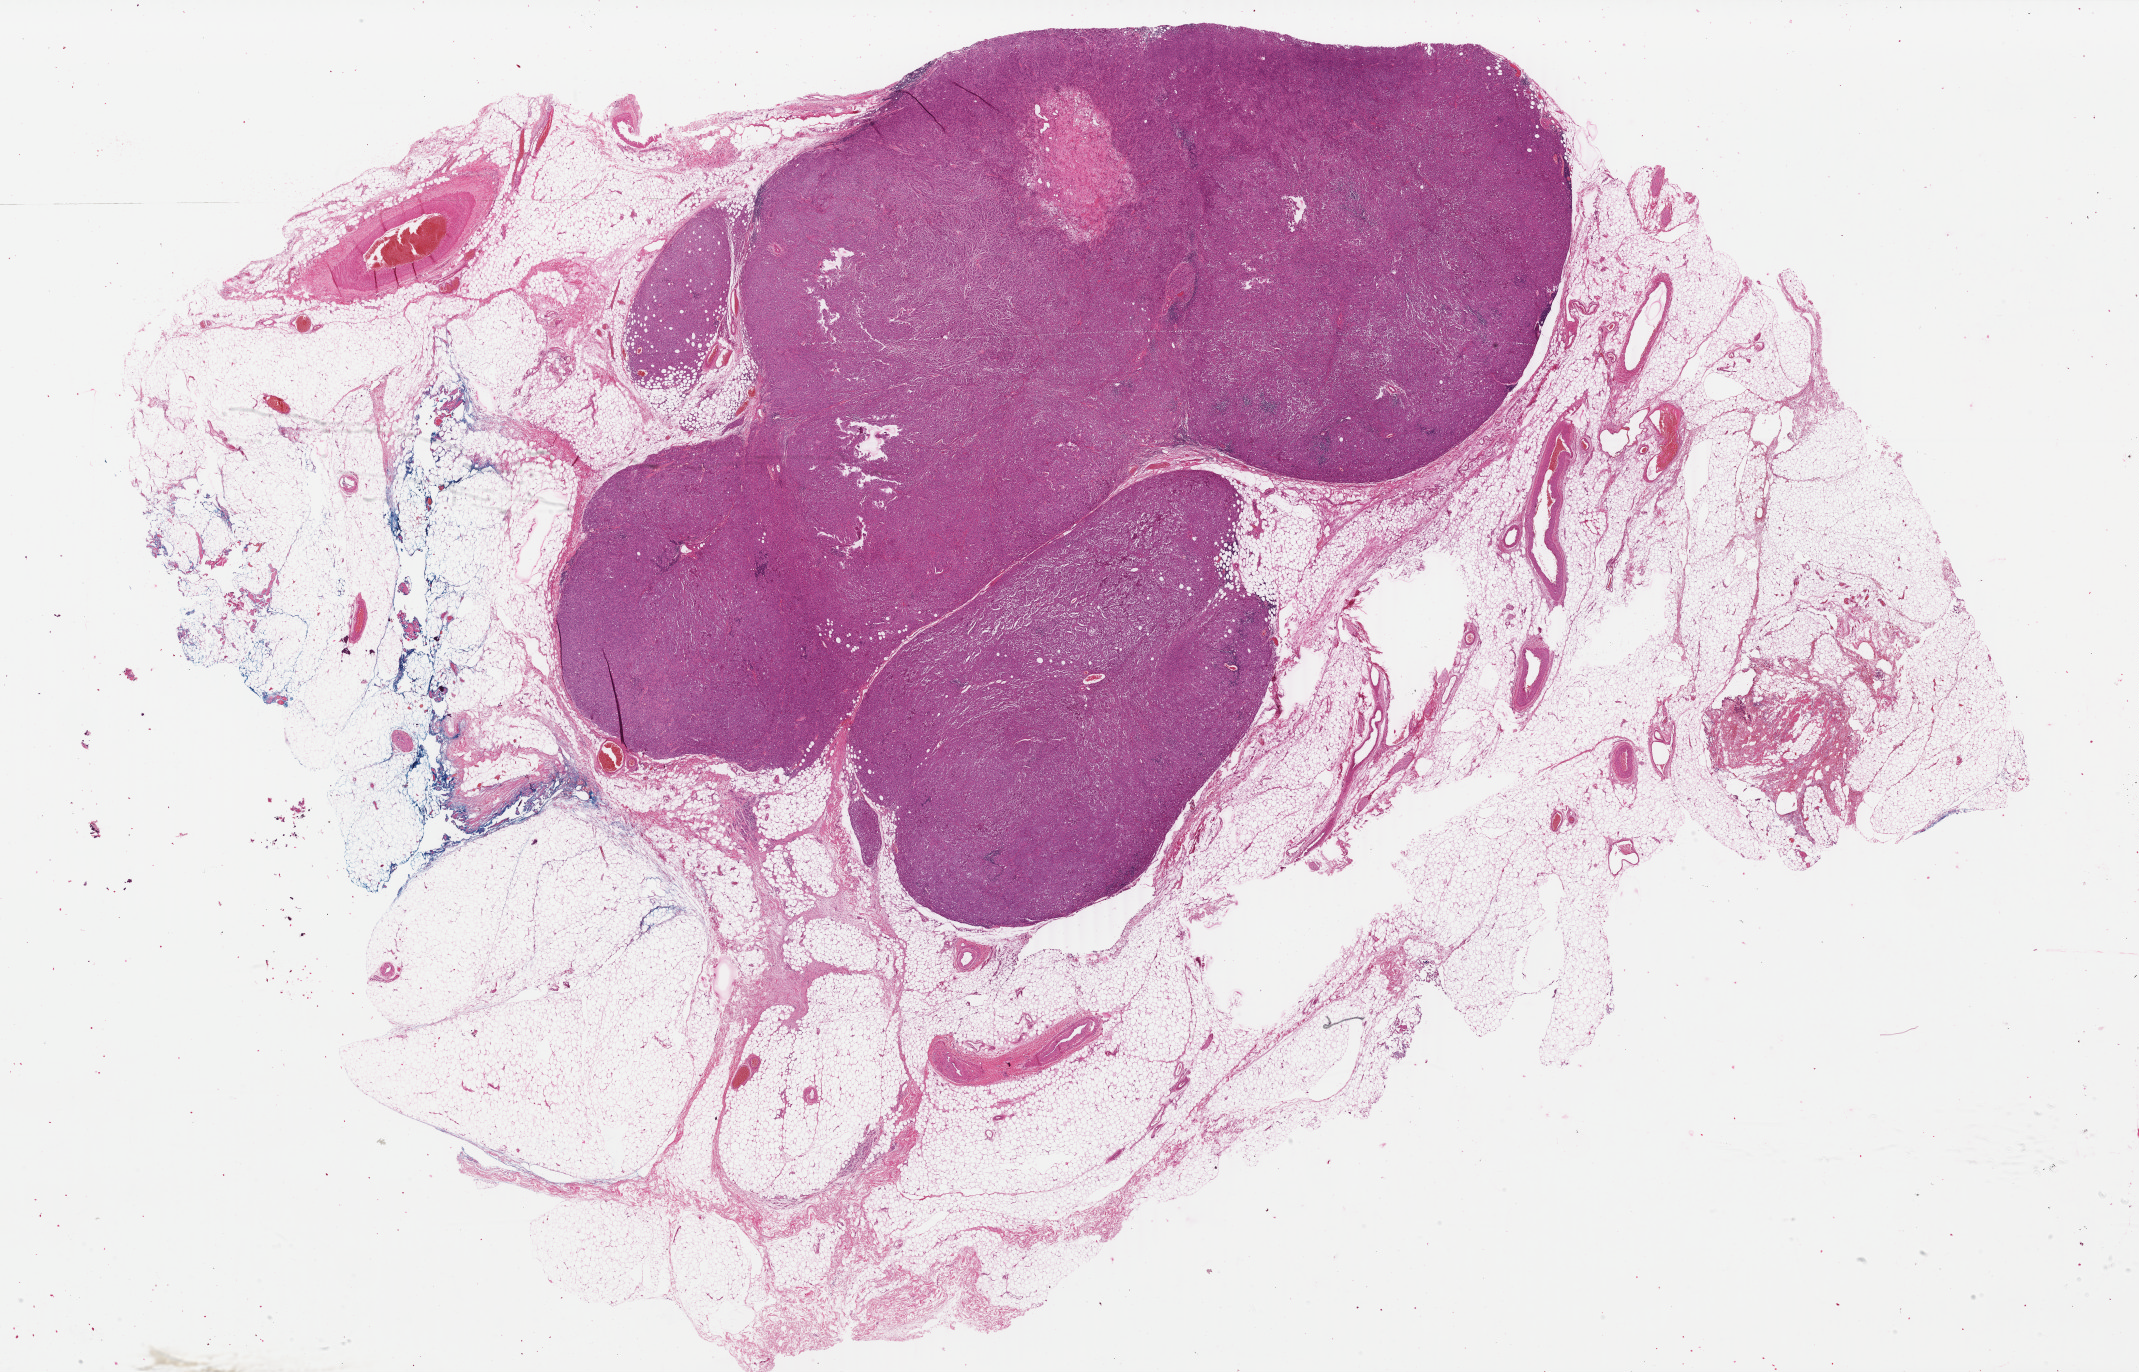
Digitized Hematoxylin and eosin (H&E) stained tissue section (whole slide), low-resolution overview of the scanned area, about 34.0 x 21.8 mm. Formalin-fixed paraffin-embedded (FFPE) diagnostic section. Skin, primary tumour sample. Male, age 79 years at initial diagnosis.
Pathologic diagnosis: Malignant melanoma, NOS.